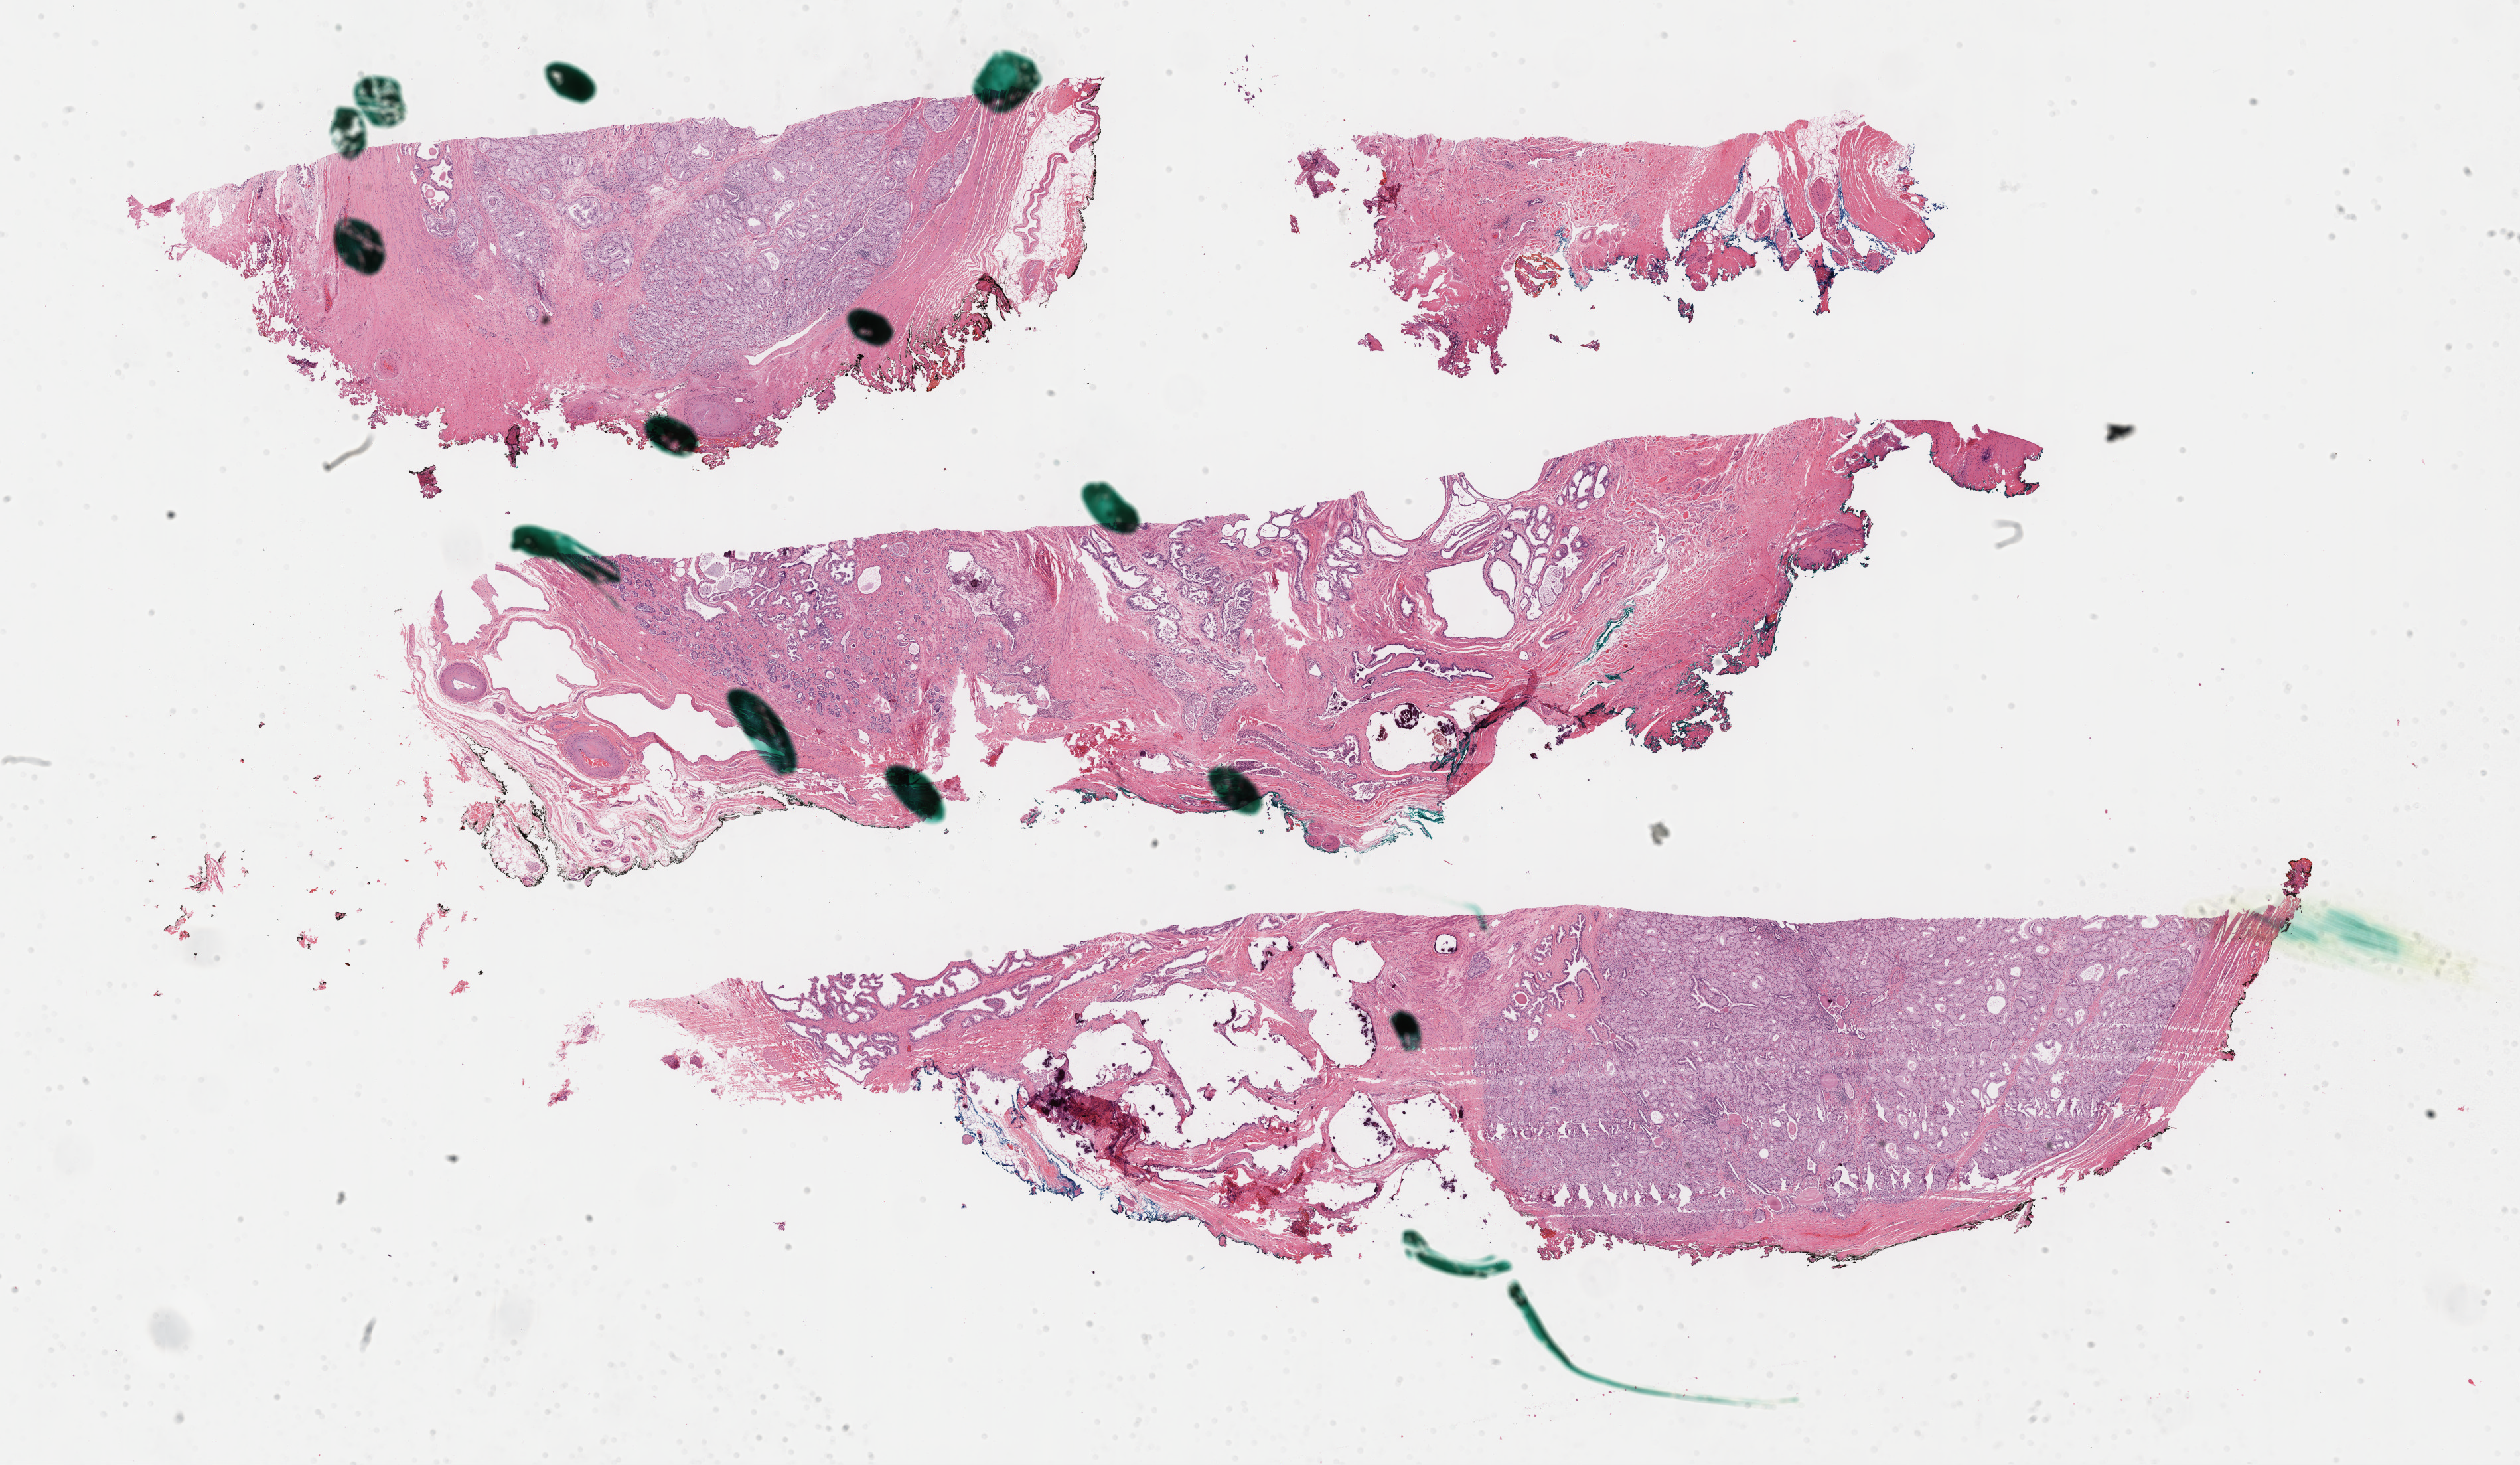
Whole-slide histology image, H&E — low-resolution overview of the scanned area, about 30.7 x 17.8 mm, formalin-fixed paraffin-embedded (FFPE) diagnostic section, primary tumour sample from the prostate. Patient: male, age at initial diagnosis 65 years. Gleason score: 6 (3+3).
- diagnosis: Adenocarcinoma, NOS (prostate gland)